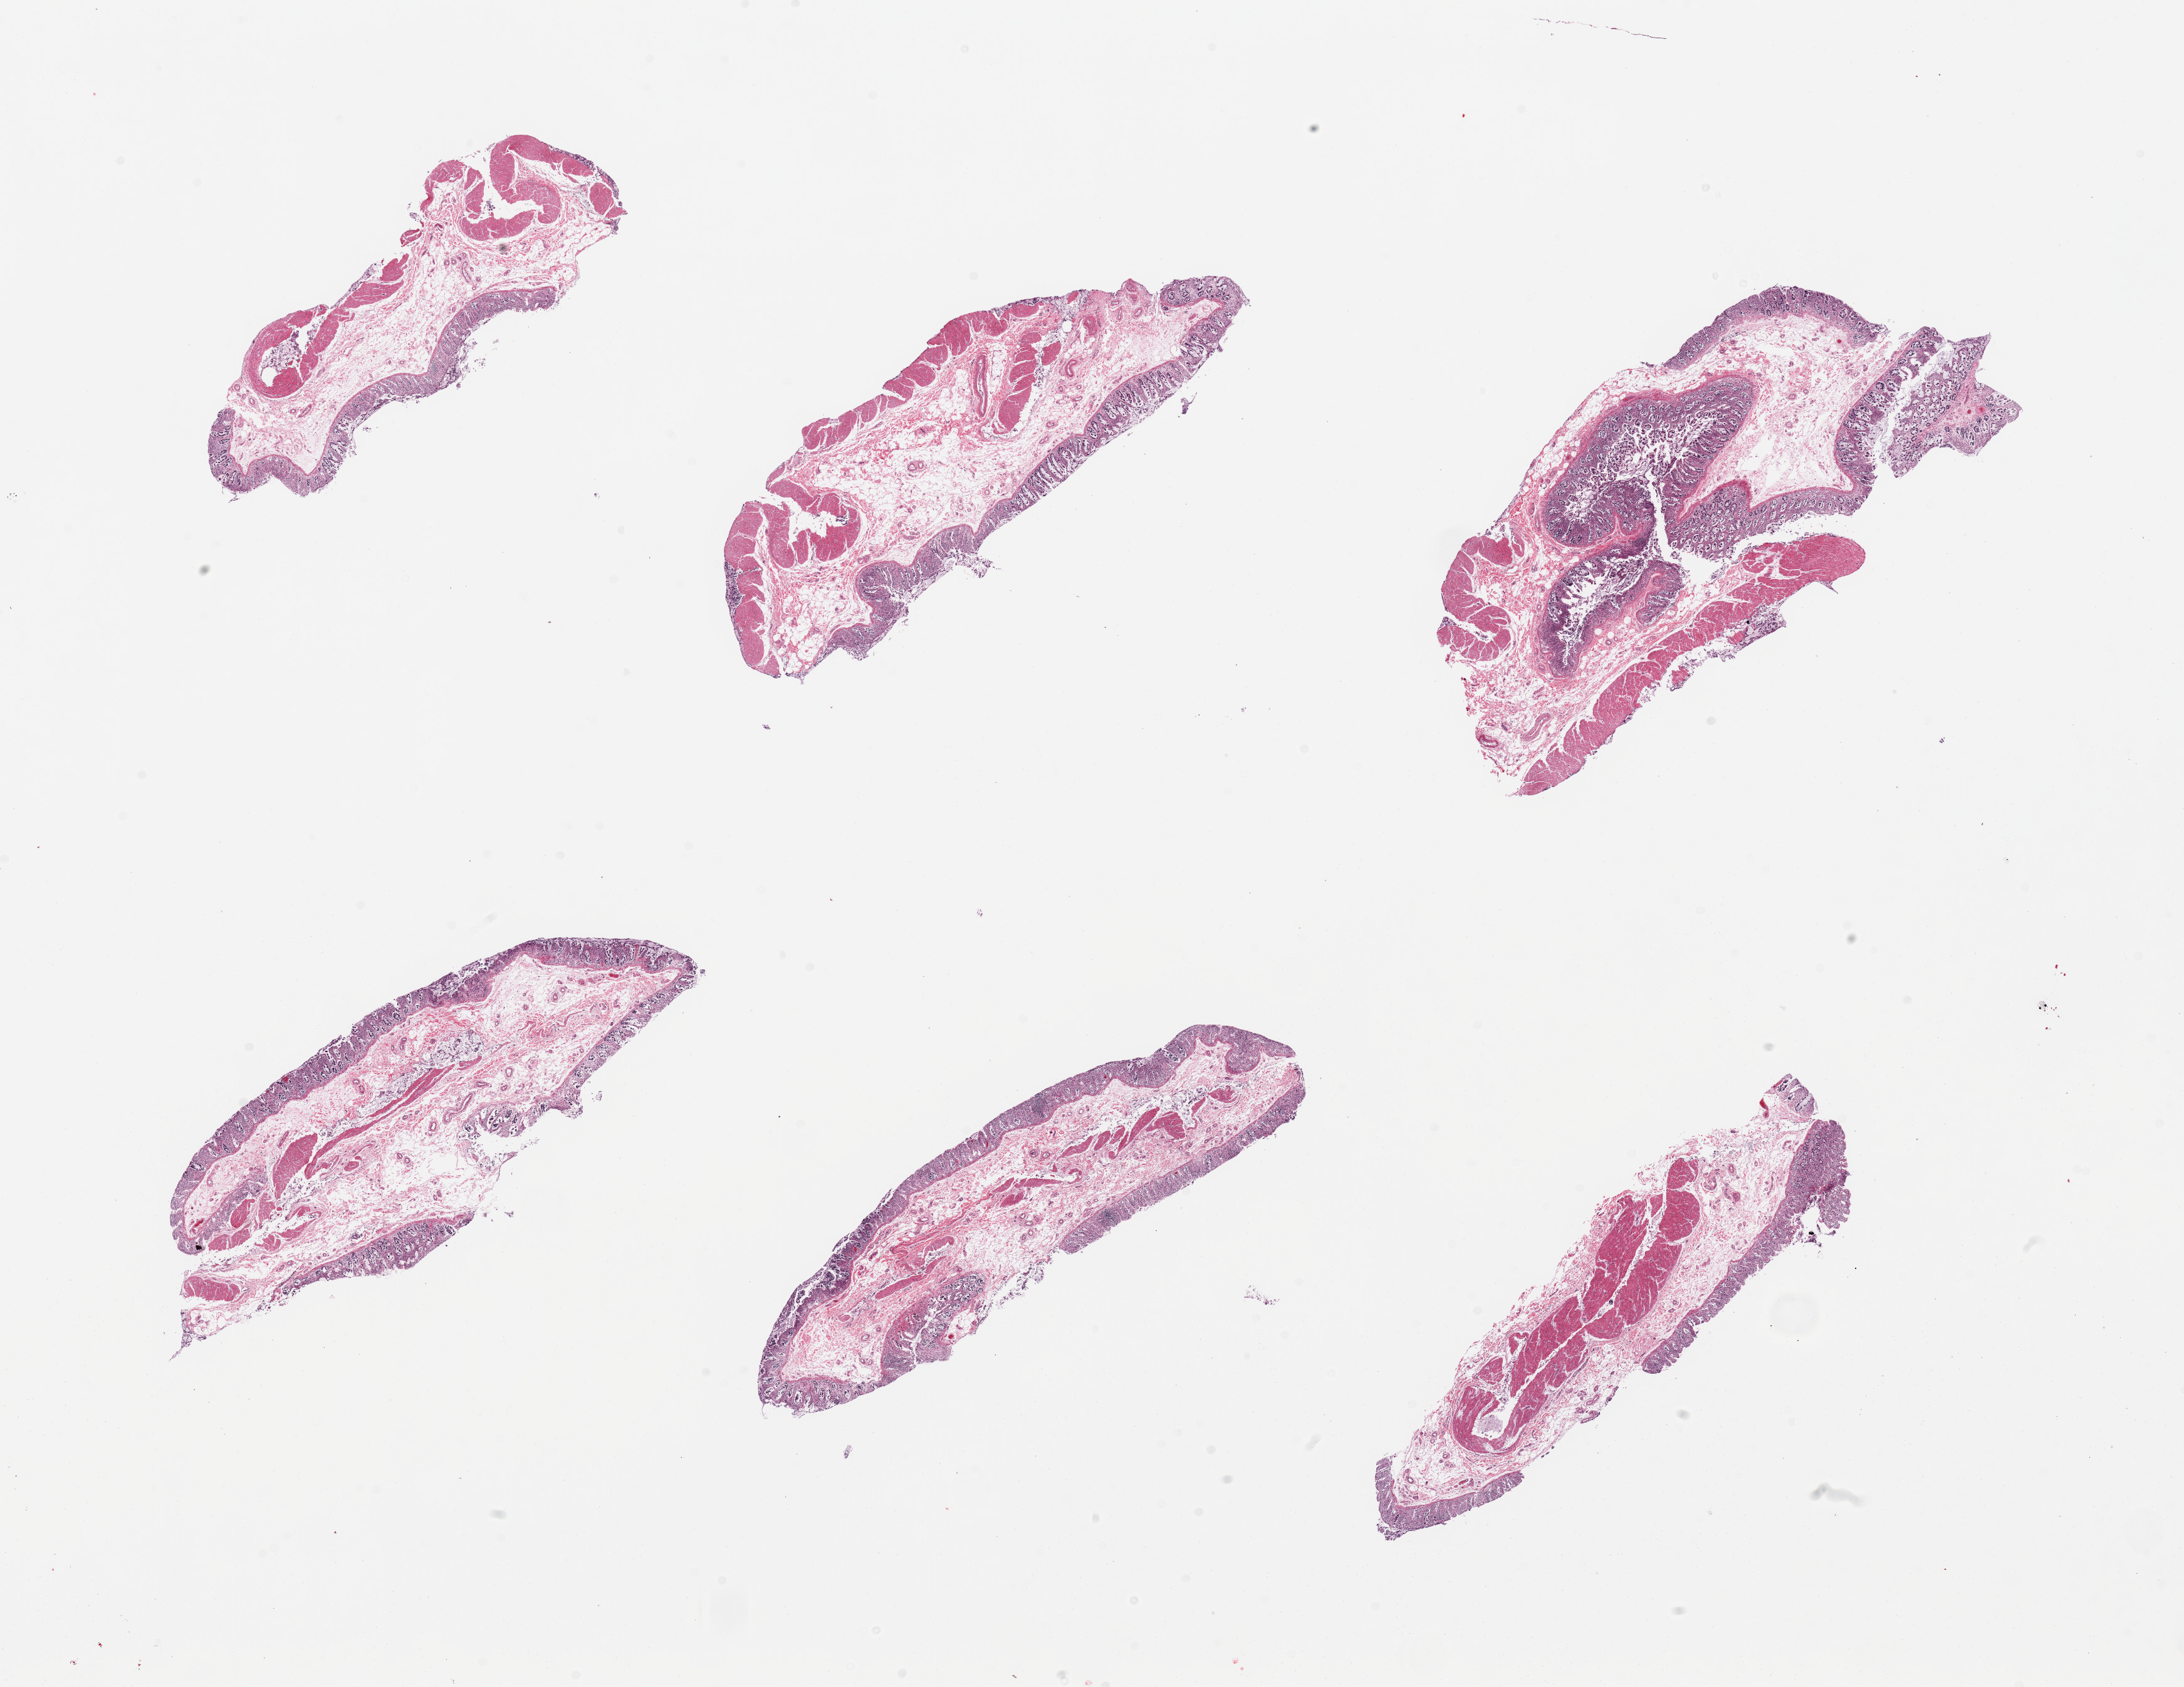
Whole-slide image, H&E stain, brightfield — a low-resolution overview of the entire scanned area, about 27.6 x 21.3 mm, PAXgene-fixed, paraffin-embedded tissue, sampled site (target tissue): transverse colon, donor tissue sample. Male donor.
Review note (as recorded): 6 pieces, epithelial component of mucosa completely autolyzed.